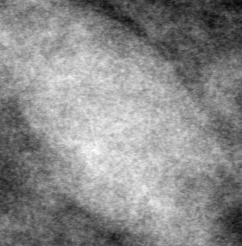
Region of interest cut from a scanned film mammogram (one marked finding); left breast; CC view; BI-RADS breast density category 1 (scale 1–4).
Mass, shape oval, margins obscured; BI-RADS assessment category 0; pathology result (as recorded, not read from the image): benign.